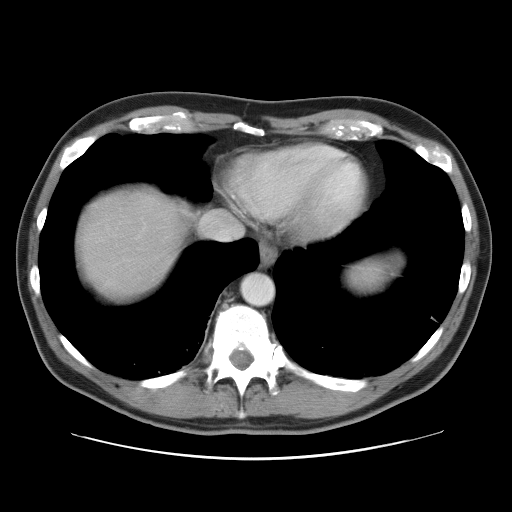
Contrast-enhanced abdominal CT, one axial slice; position 48 of 52 along the scan axis; reconstruction kernel STANDARD; 120 kVp; intravenous contrast given; soft-tissue window (W 400 / L 40 HU); 5 mm slice thickness; 512 × 512 image matrix. Male patient, age 70 years. From the clinical record (not read from this slice): diagnosis: colorectal cancer liver metastases, imaged before liver resection; multiple liver metastases: yes; largest metastasis: 4 cm.
Annotated regions visible in this slice (manually delineated by an expert):
- hepatic veins: bounding box [x1, y1, x2, y2] px = [202, 193, 250, 223]
- liver: [76, 186, 186, 304]